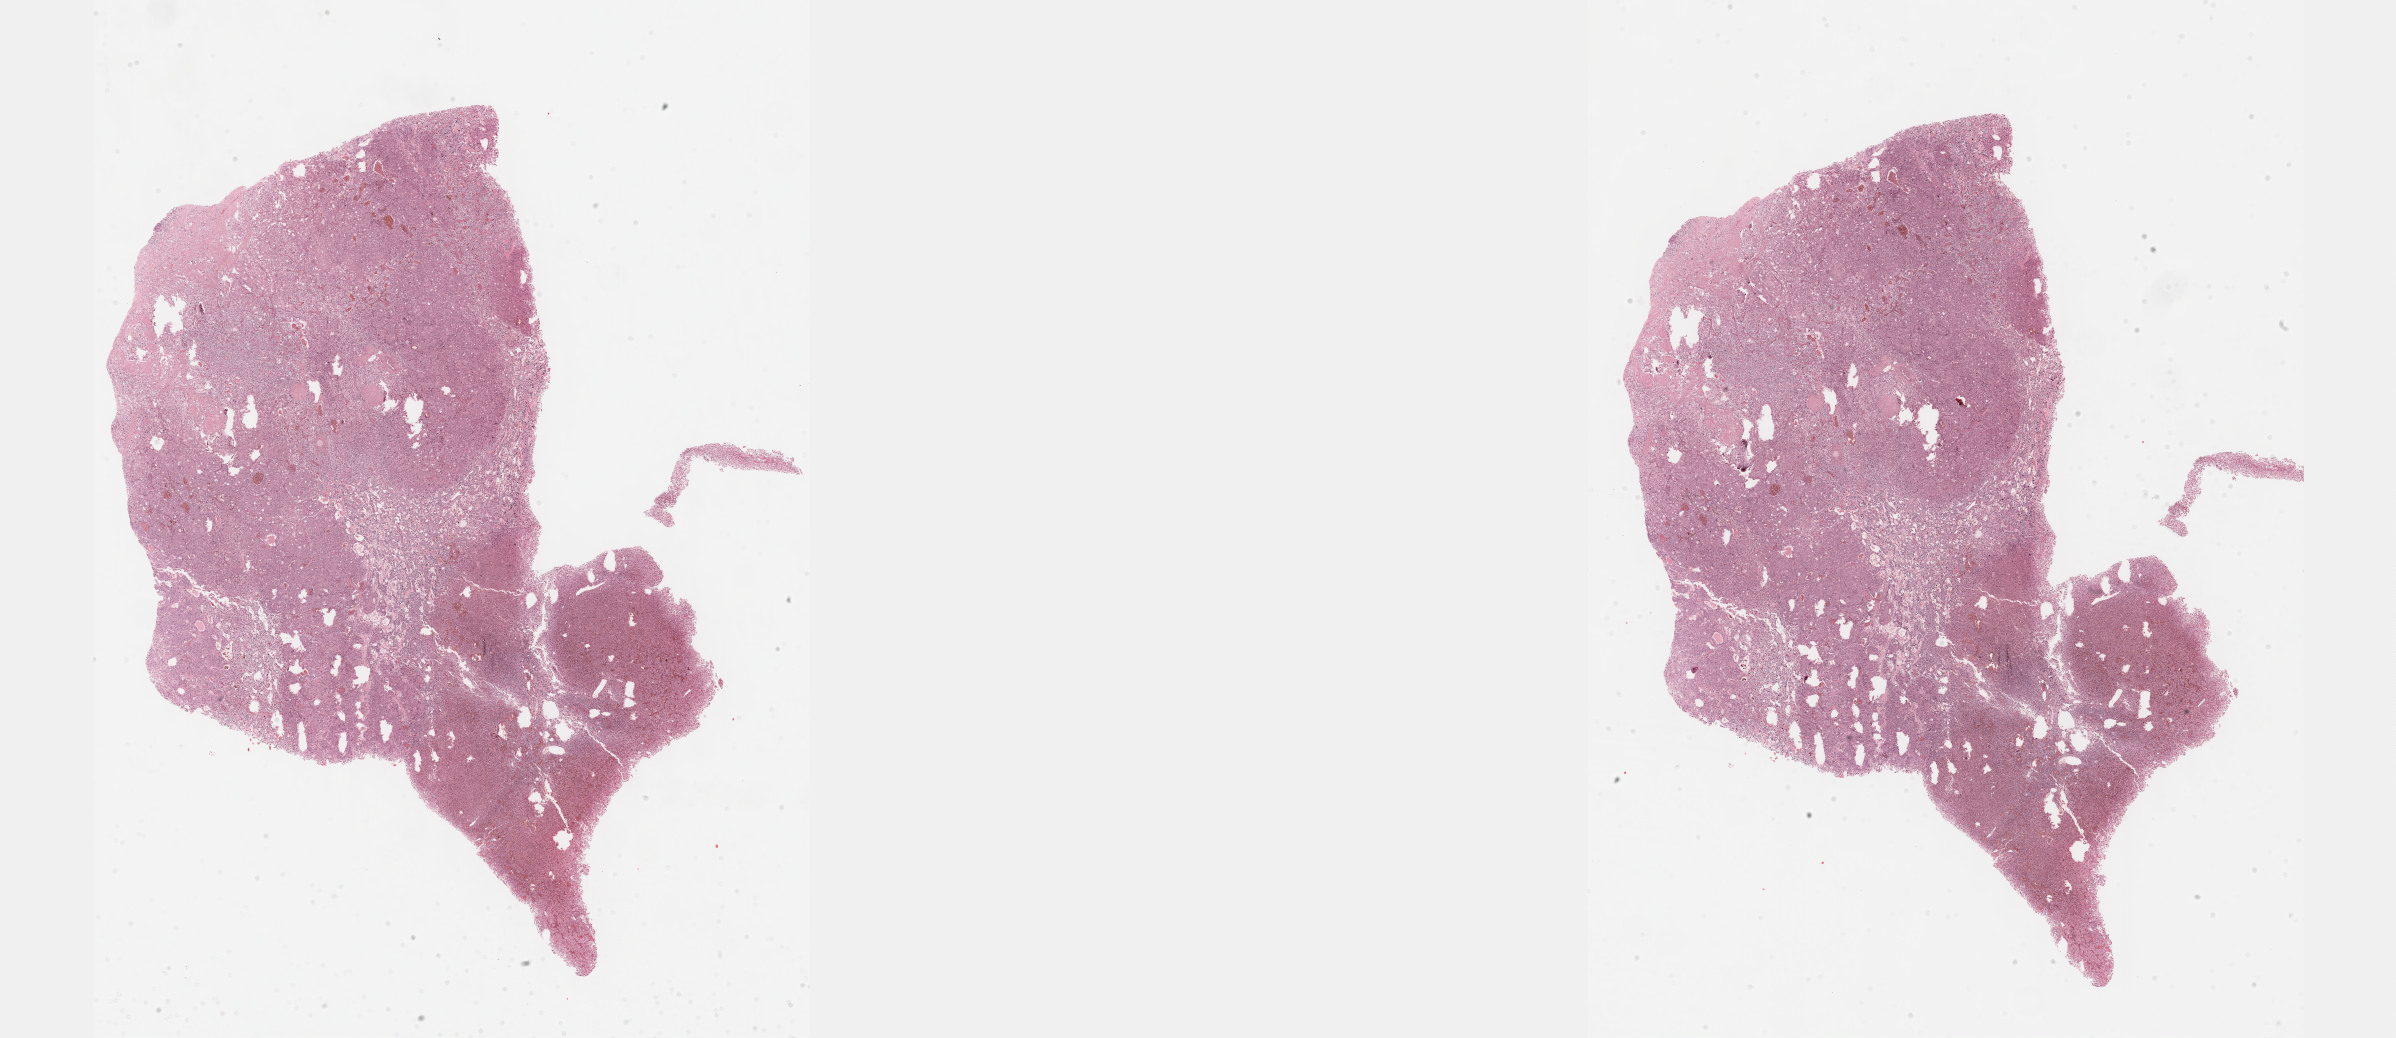
Whole-slide histology image, Hematoxylin and eosin (H&E) stained — shown as a low-resolution overview of the whole scanned area (about 38.7 x 16.8 mm, slide scanned at 40x); formalin-fixed paraffin-embedded (FFPE) diagnostic section; primary tumour sample from the retroperitoneum and peritoneum. Patient: male, age at initial diagnosis 44 years.
Pathologic diagnosis: Extra-adrenal paraganglioma, NOS (retroperitoneum).